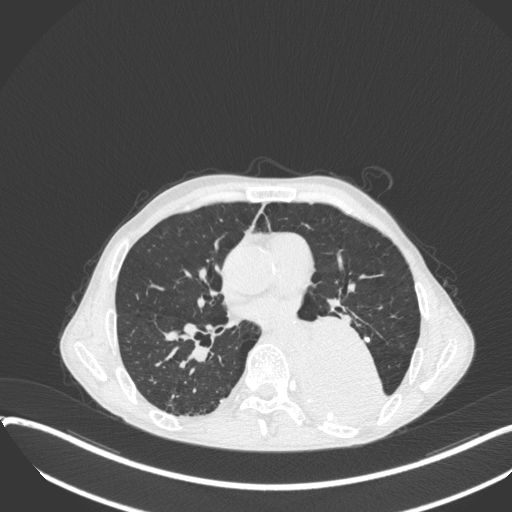
Chest CT, one axial slice. Position 188 of 400 along the scan axis. 120 kVp. Lung window (W 1500 / L -600 HU). 1 mm slice thickness. 512 × 512 image matrix, field of view 400 × 400 mm. Male patient, age 57 years. From the clinical record (not read from this slice): clinical TNM (as recorded): T4 N0 M0.
Outlined on this slice (rectangle marked by the reading radiologist):
- lung tumour (recorded histology: squamous cell carcinoma): bounding box [x1, y1, x2, y2] px = [302, 311, 386, 420]